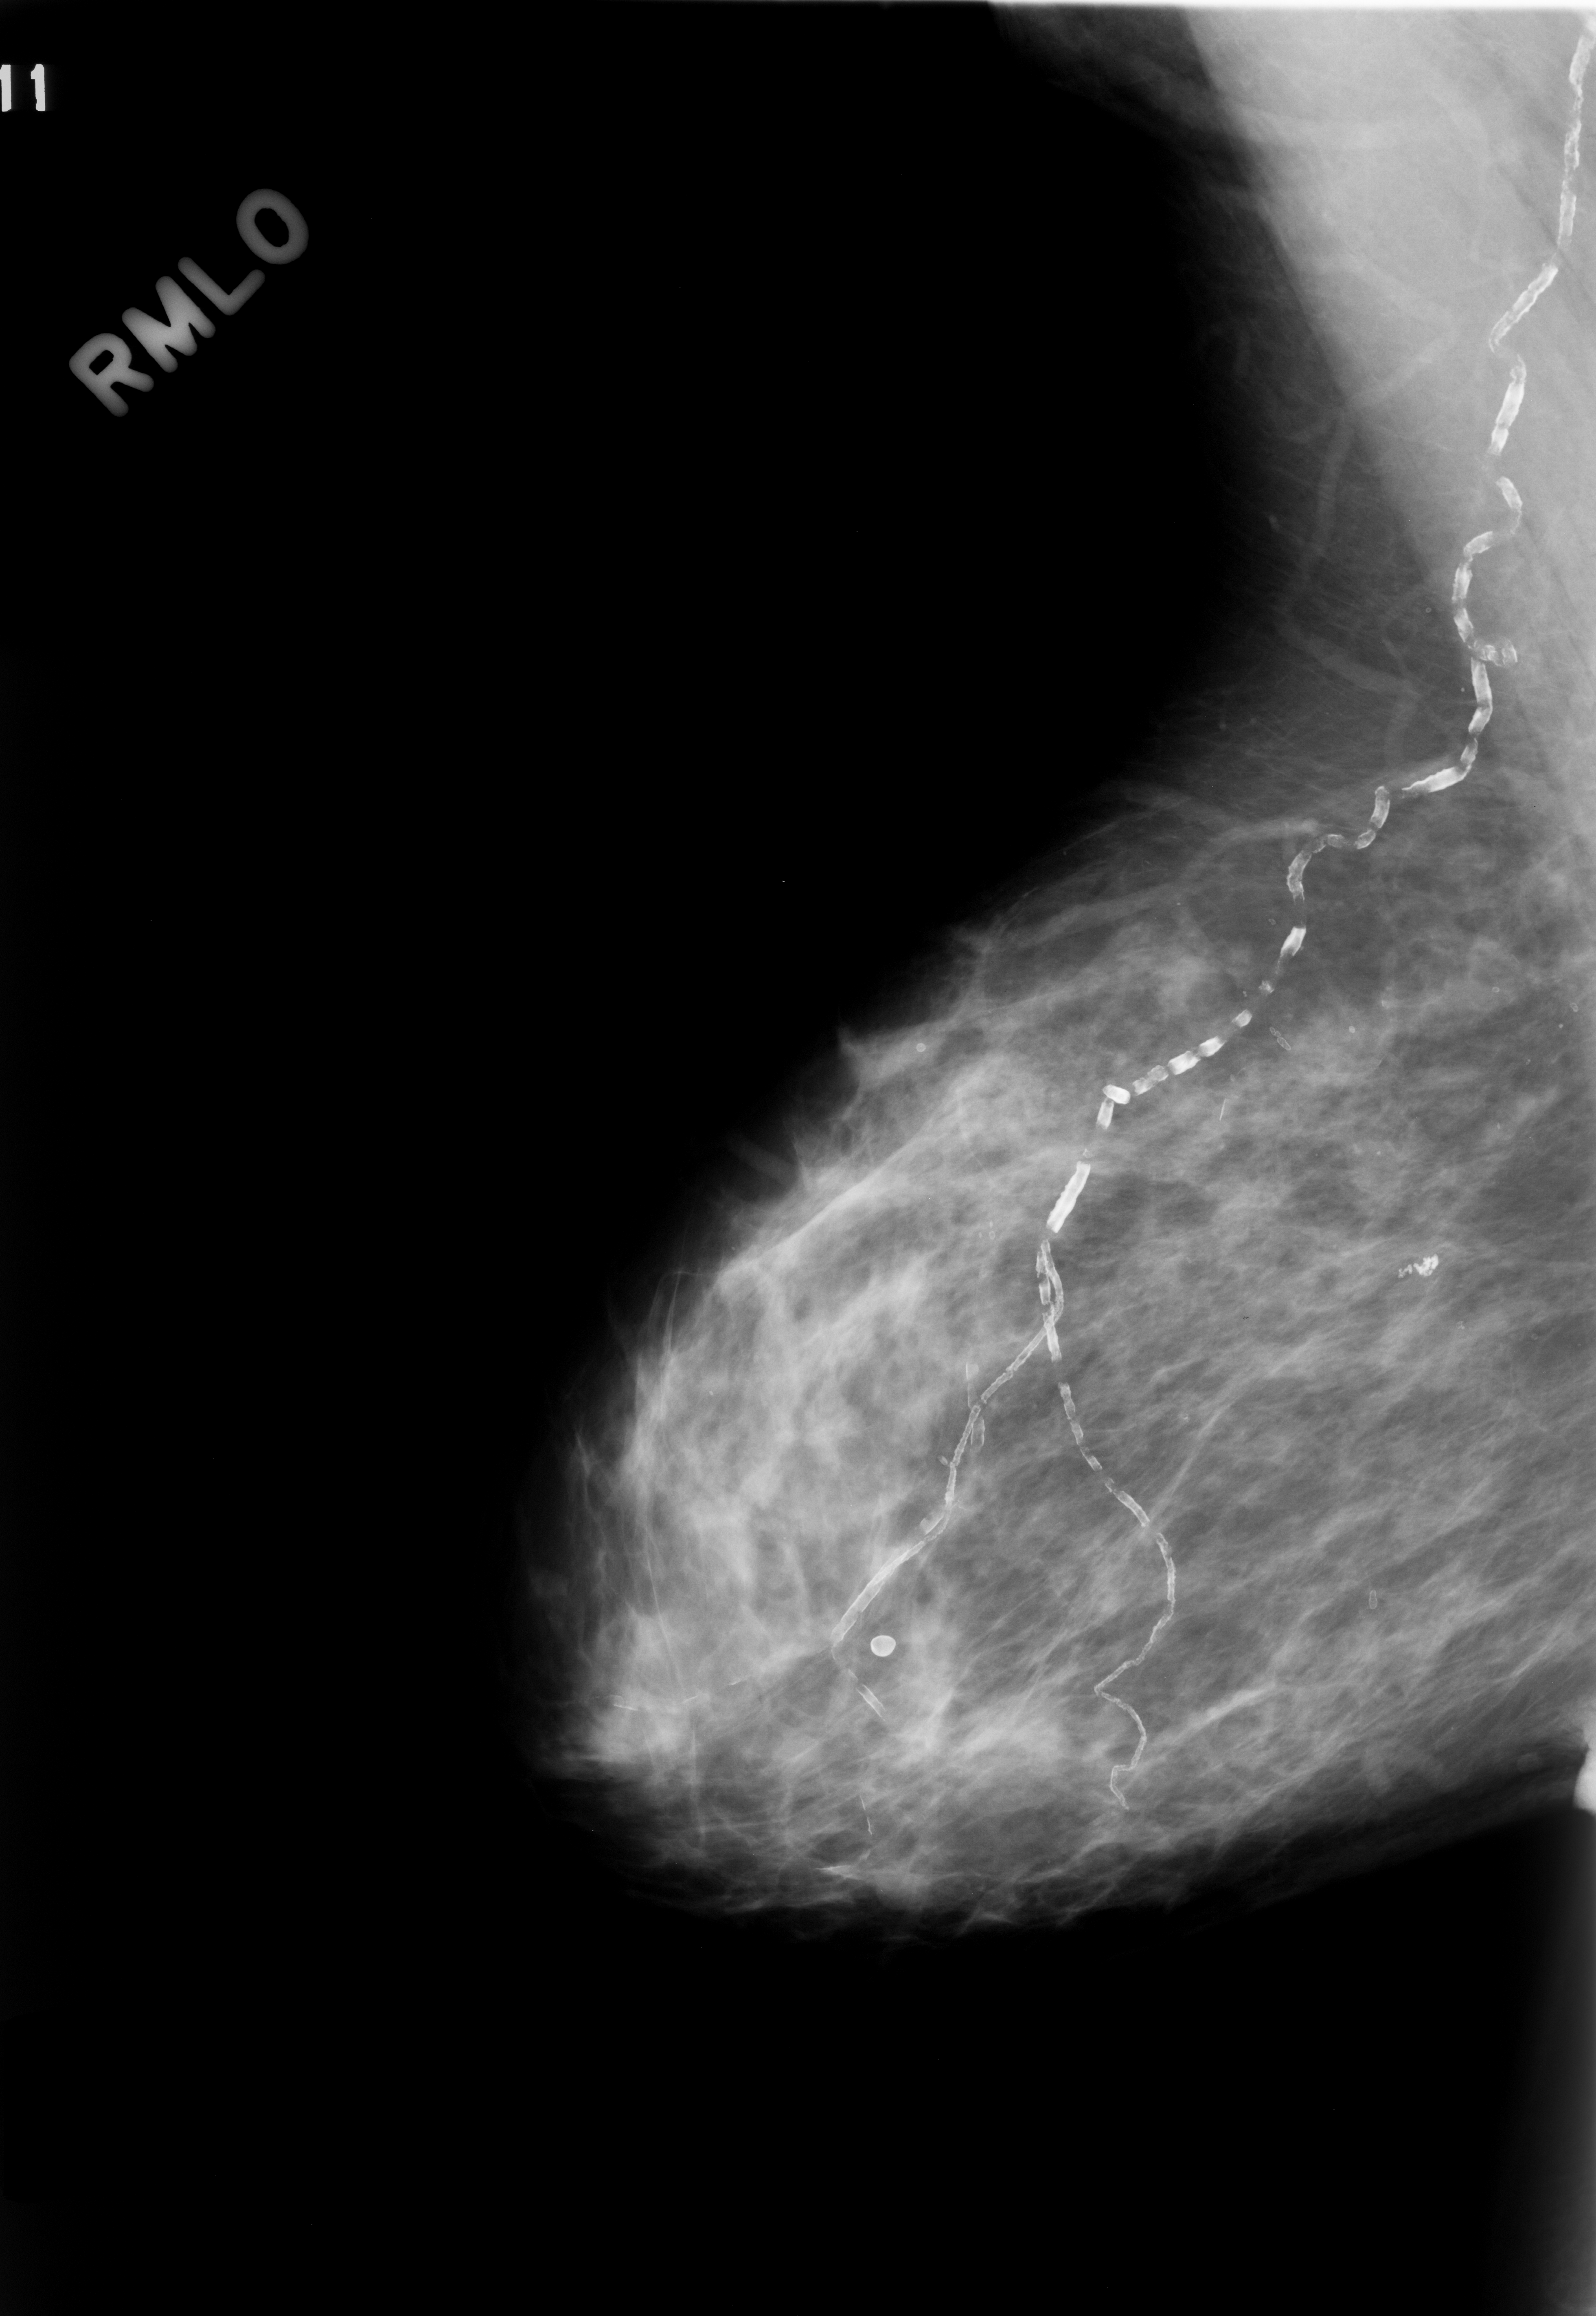
Digitized screen-film mammogram; right breast; MLO view; 1596 × 2316 image matrix.
Marked abnormalities (boxes around the expert regions of interest):
- calcifications, morphology pleomorphic, distribution clustered; BI-RADS assessment category 4; pathology result (as recorded, not read from the image): benign: bounding box [x1, y1, x2, y2] px = [1358, 1179, 1496, 1343]